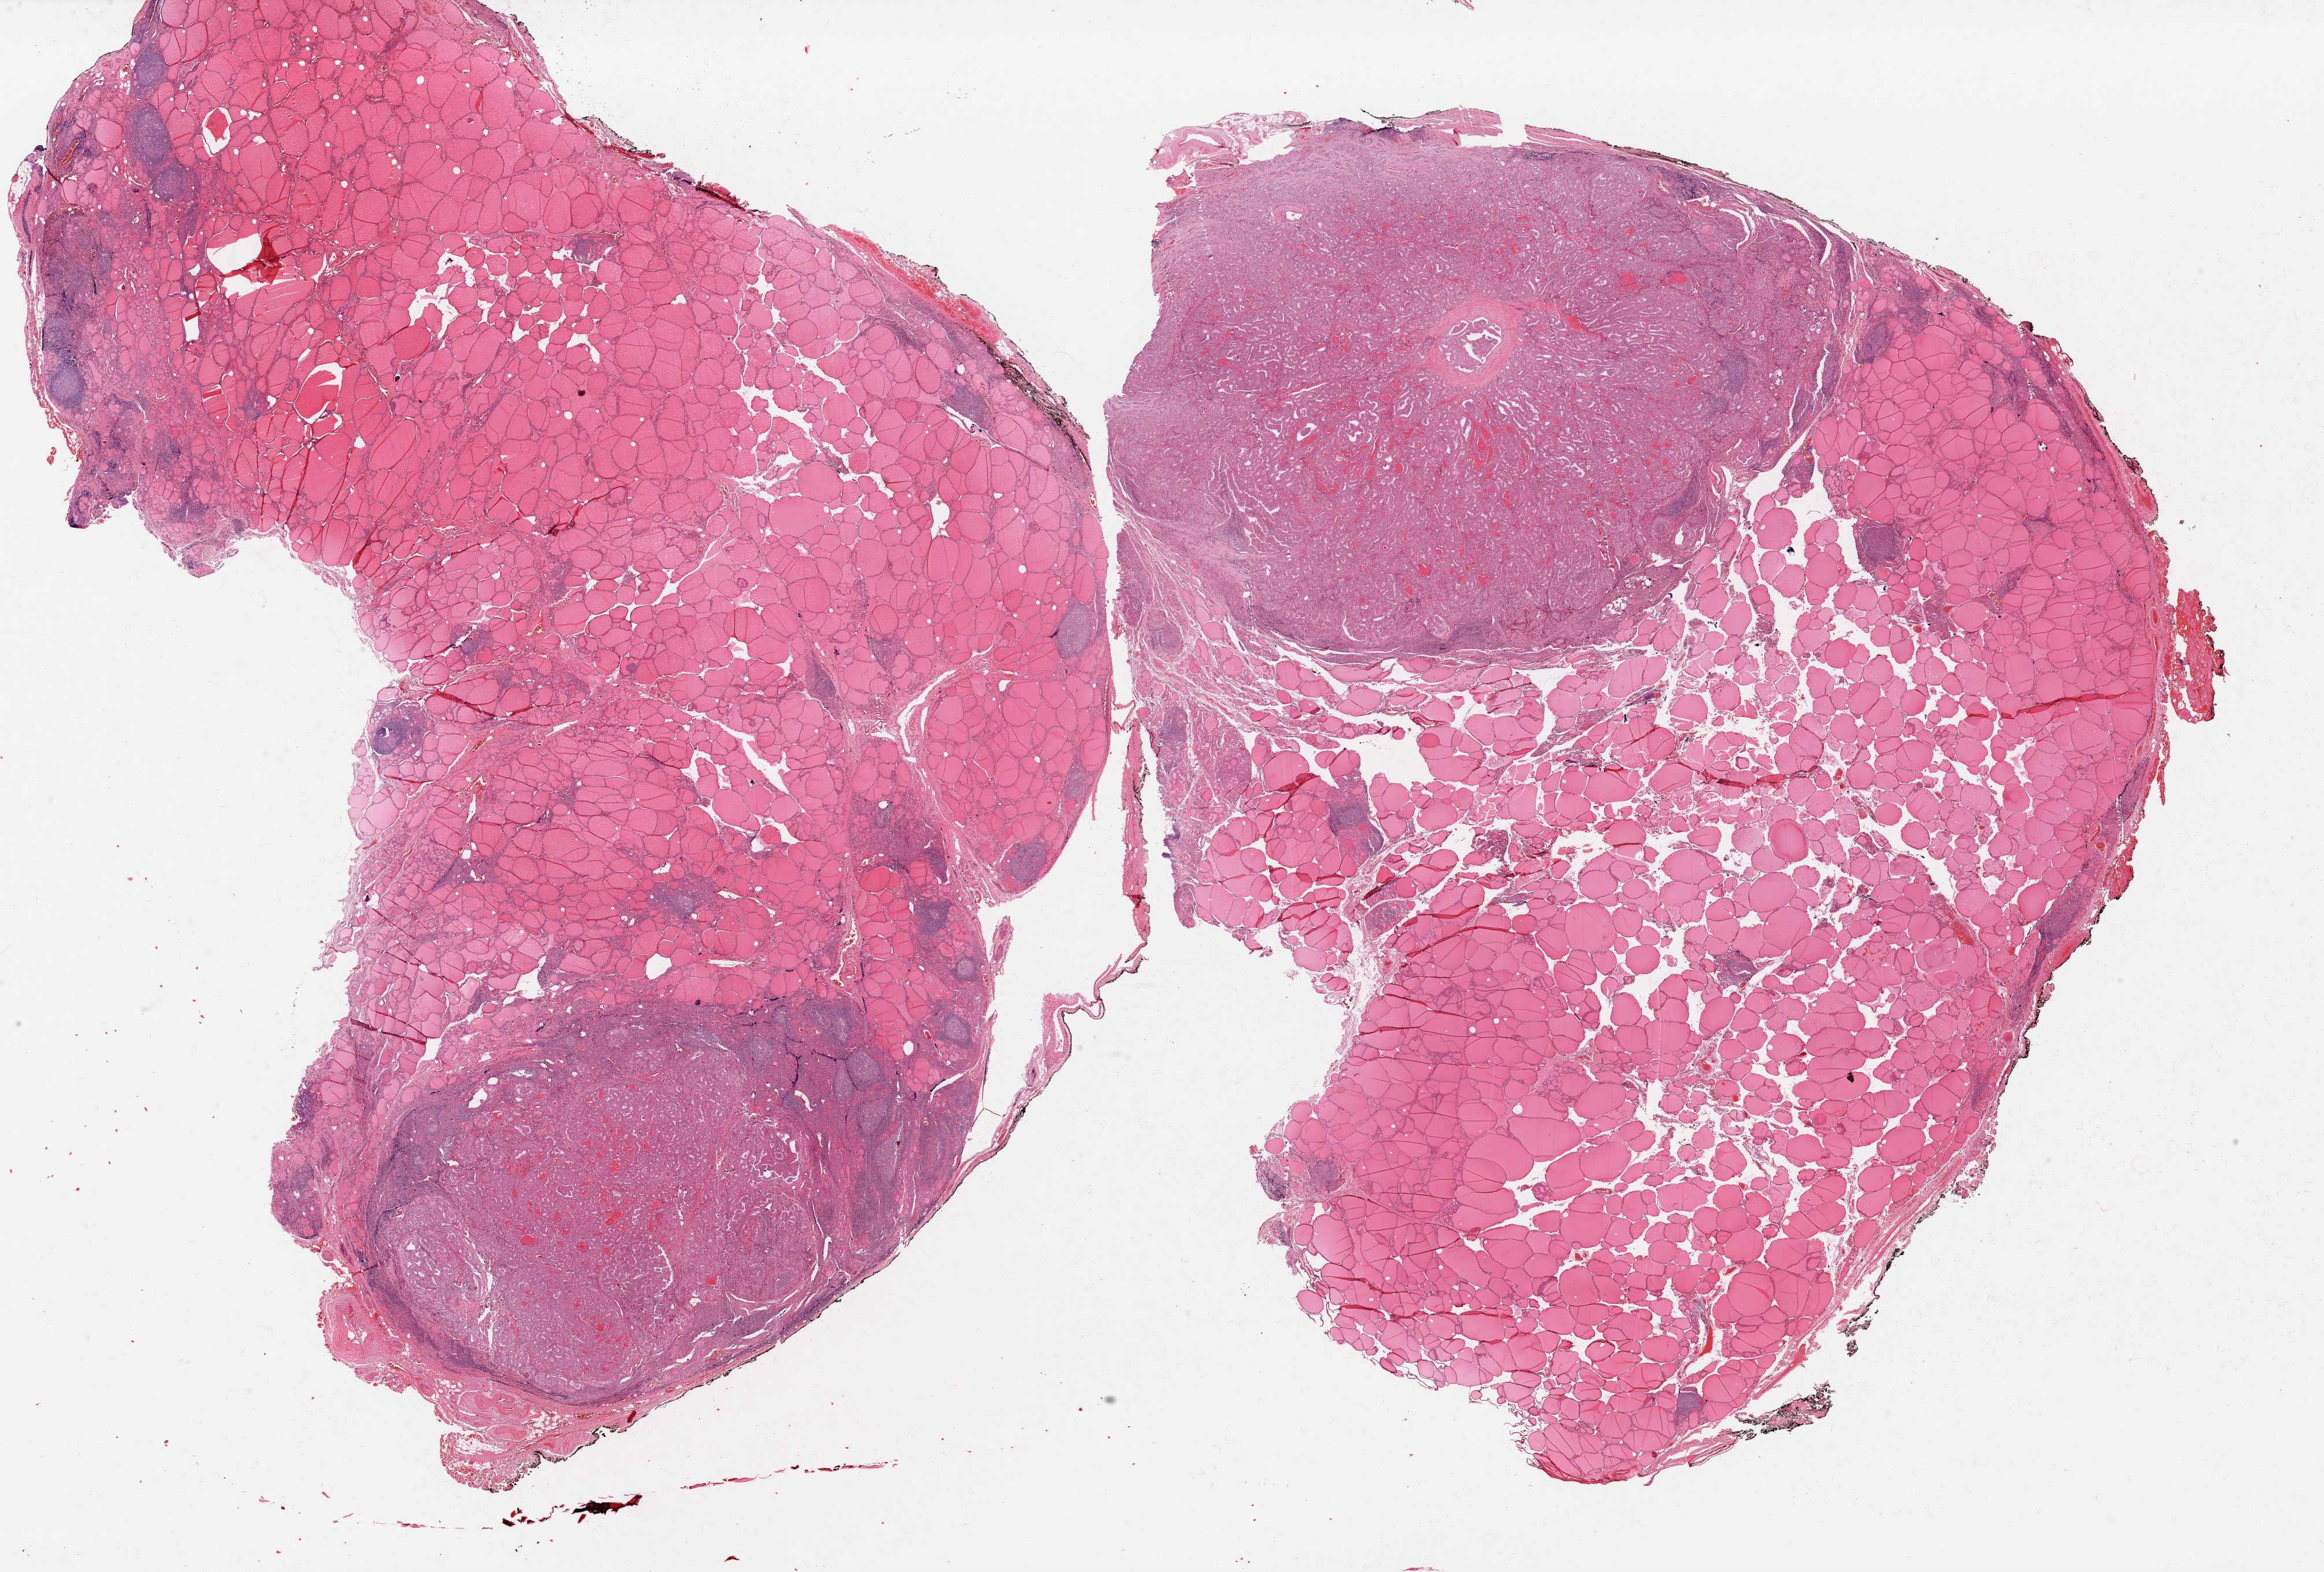
Whole-slide histology image, H&E, a low-resolution overview of the entire scanned area, about 31.7 x 21.5 mm; formalin-fixed paraffin-embedded (FFPE) diagnostic section; thyroid, primary tumour sample. Female, age 34 years at initial diagnosis.
• diagnosis: Papillary carcinoma, follicular variant
• AJCC pathologic stage: I (6th edition)
• TNM: T1 N1a MX